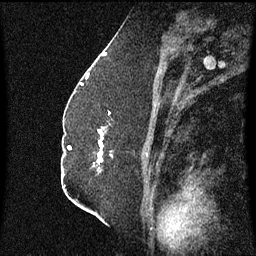
Breast MRI (dynamic contrast-enhanced), one sagittal slice; slice 35 of 60 in the series (ordered by position); dynamic contrast-enhanced series, image 2 of 3 at this slice position (ordered by acquisition); 1.5 T; TE 4.2 ms, TR 8.4 ms; 2.3 mm slice thickness; 256 × 256 image matrix, field of view 200 × 200 mm. Female patient, age 52 years. From the clinical record (not read from this slice): setting: breast cancer imaged before/during neoadjuvant chemotherapy; receptor status: HR-positive, HER2-negative.
Annotated regions visible in this slice (semi-automatically segmented with operator editing):
- analysis volume of interest (the breast-tissue region the enhancement analysis was run in; not a lesion): bounding box (x1, y1, x2, y2) in pixels: (97, 130, 112, 165)
- tumour enhancement mask (voxels above the 70 % enhancement threshold inside the analysis volume of interest): (97, 130, 103, 165)